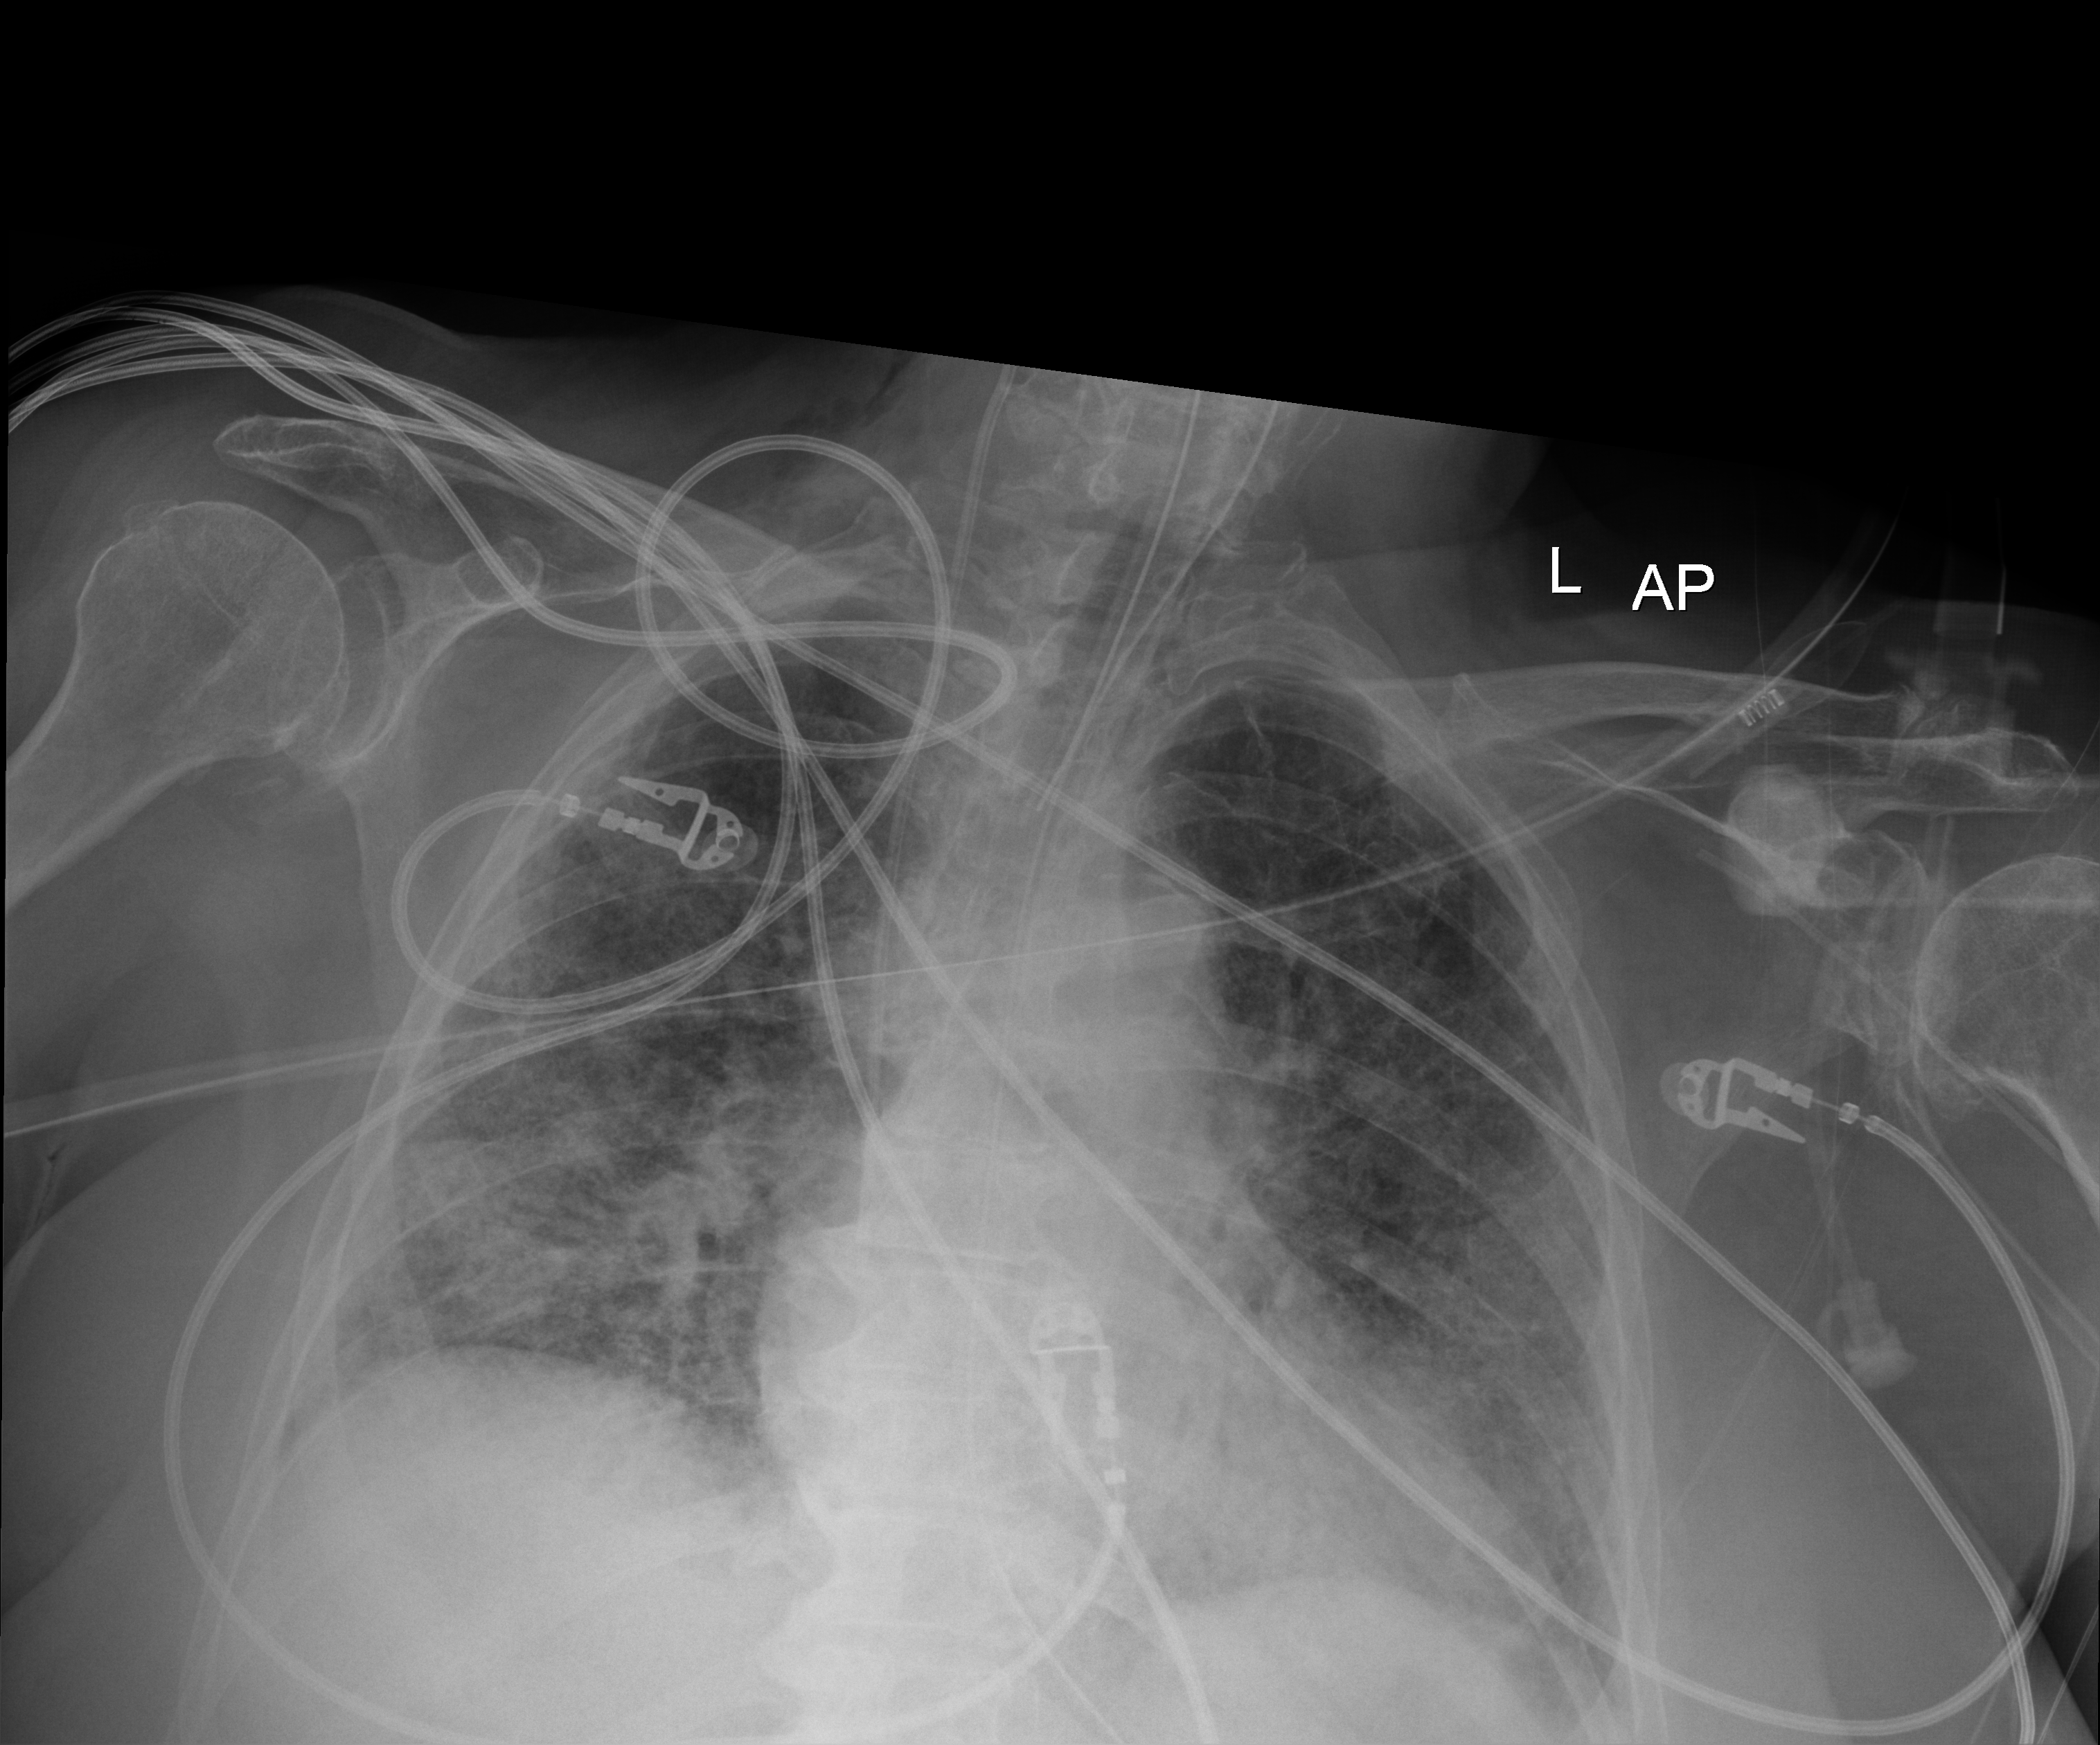
Portable chest radiograph; anteroposterior (AP) projection. Female patient hospitalised with COVID-19, age 75–90 years.
Admission-level facts for this patient (not findings on this image; timing relative to this image not recorded): admitted to intensive care during this hospital stay: no; hypertension (admission record): no; smoking status (admission record): former.